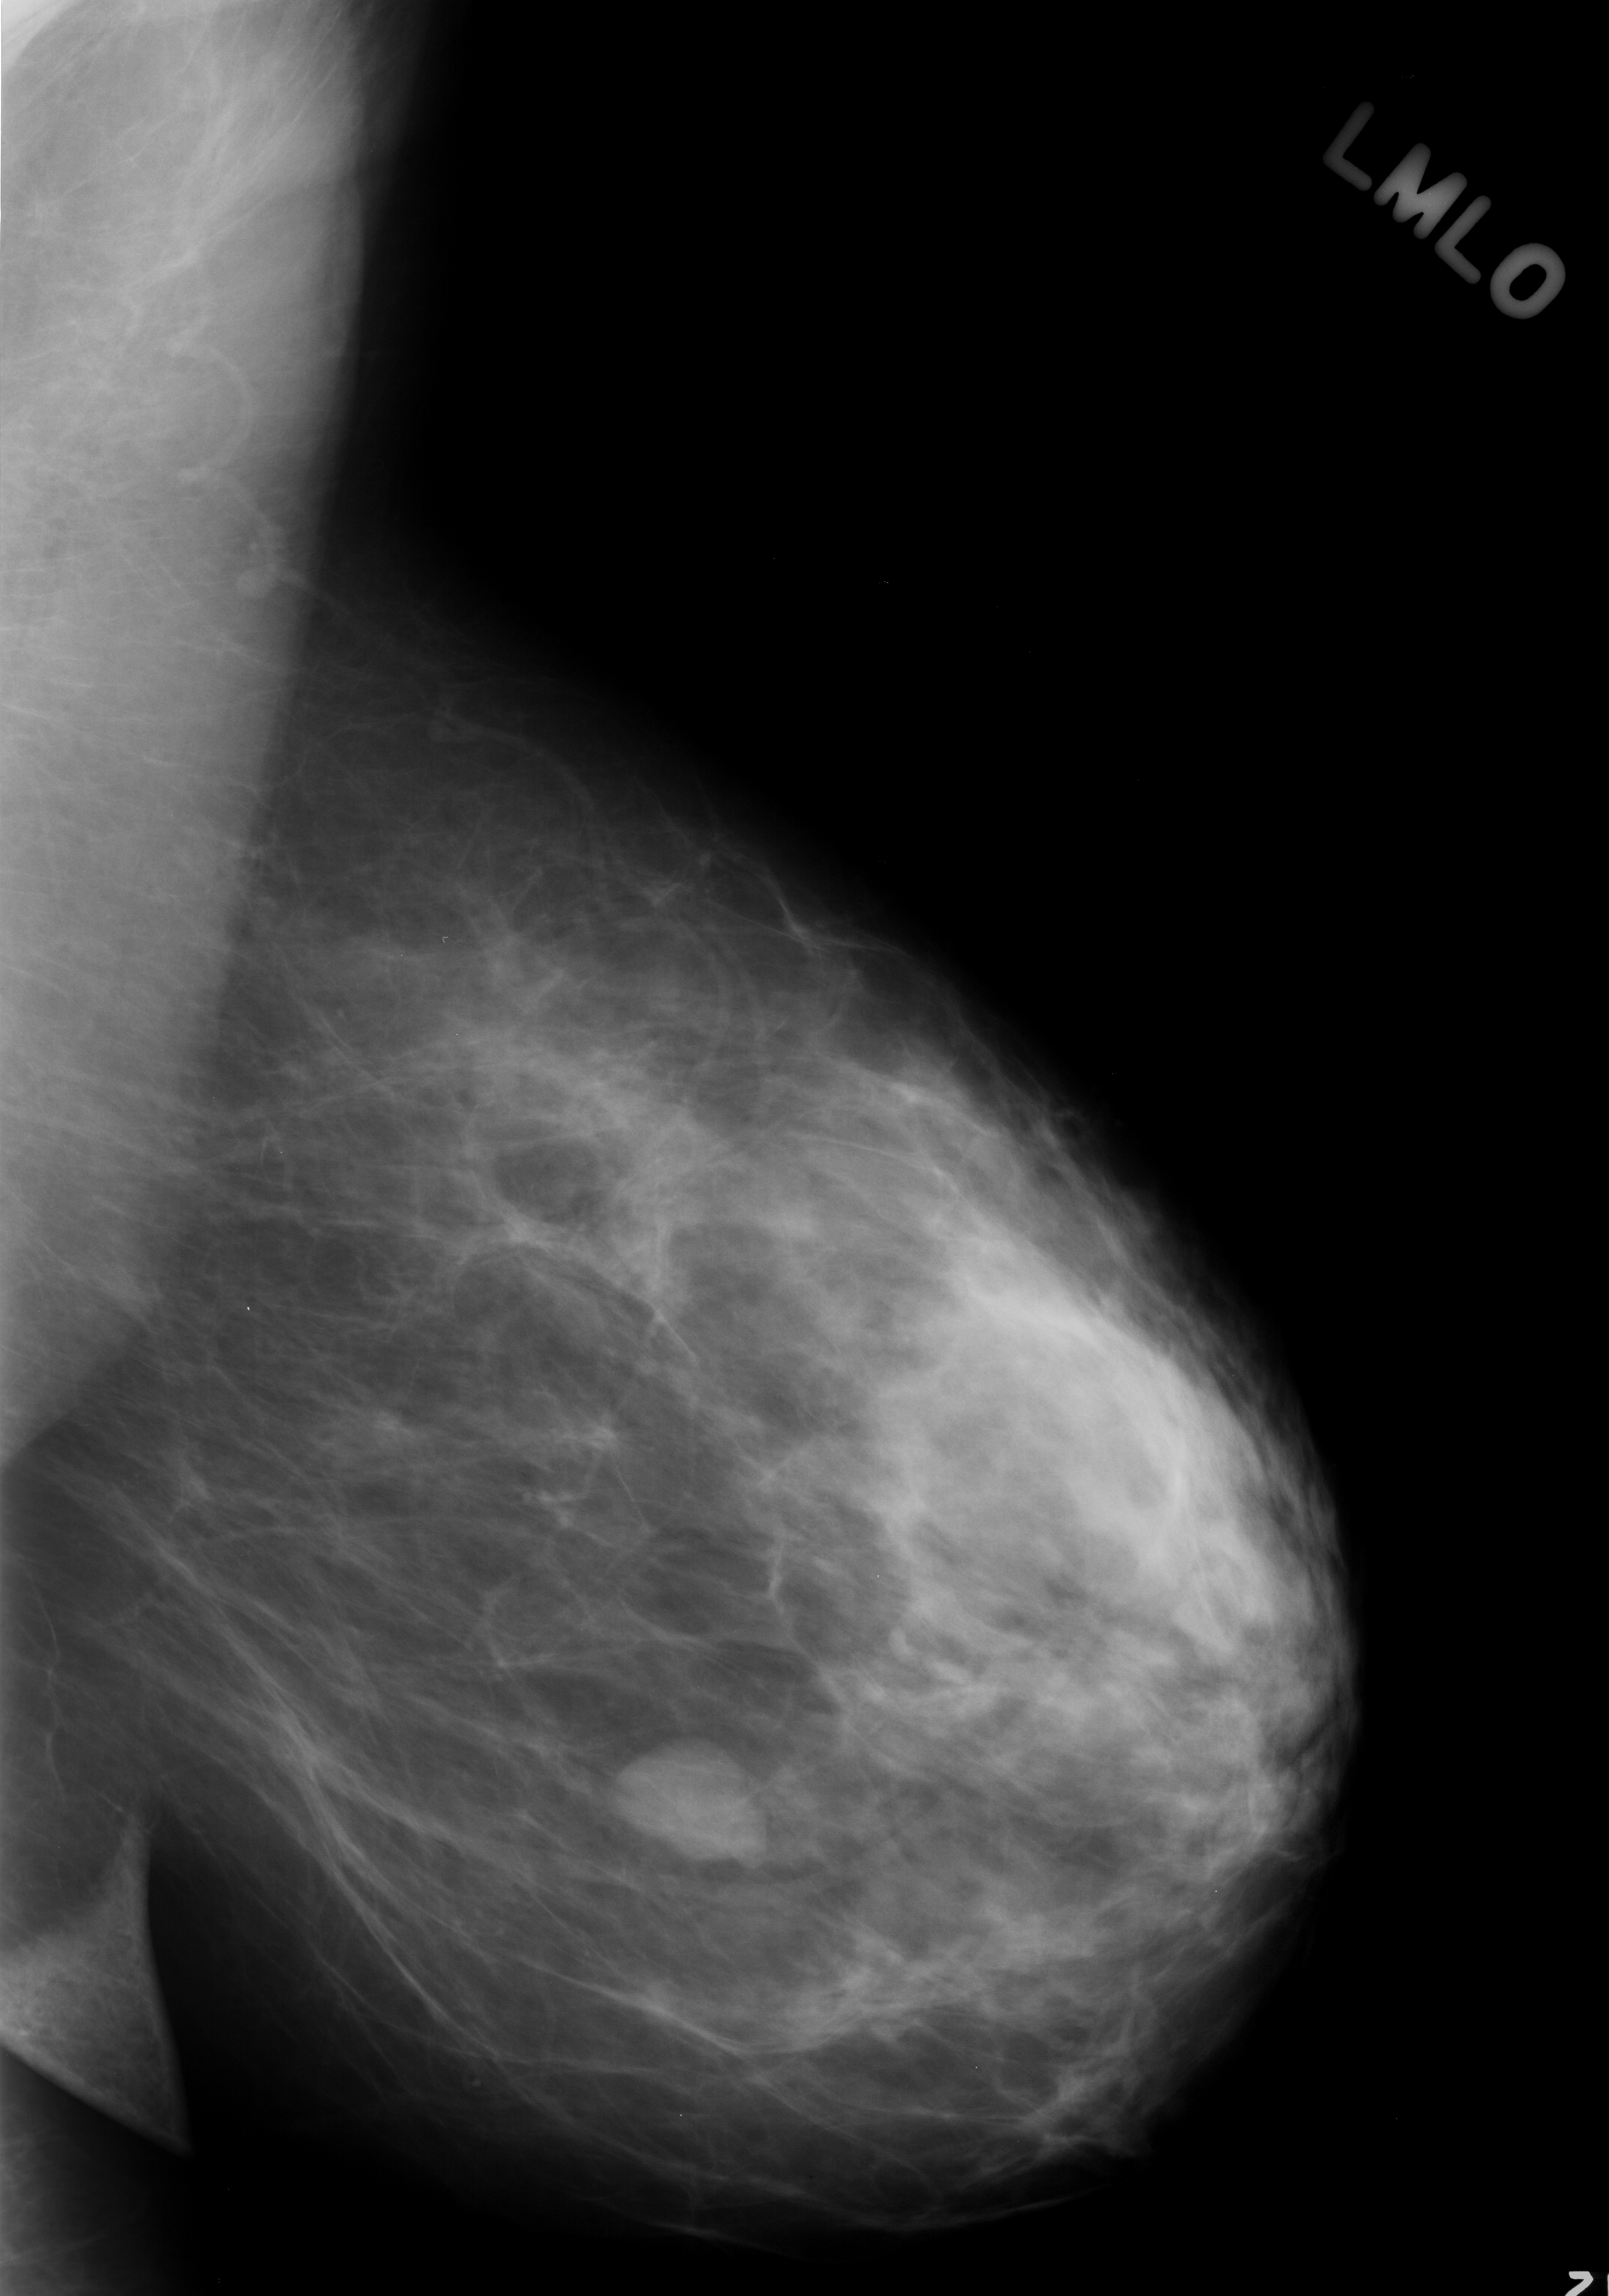
Digitized screen-film mammogram; left breast; MLO view.
Marked abnormality: mass, shape lobulated, margins circumscribed; BI-RADS assessment category 3; pathology (as recorded): benign.